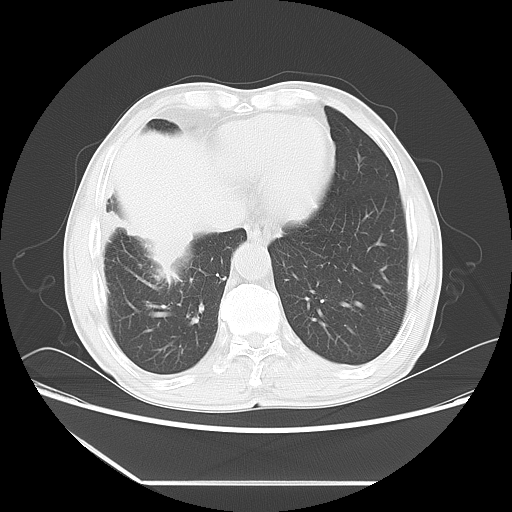
Chest CT, one axial slice; position 18 of 60 along the scan axis; reconstruction kernel LUNG; lung window (W 1500 / L -600 HU); 512 × 512 image matrix, field of view 386 × 386 mm. Patient: male, 72 years. From the clinical record (not read from this slice): clinical TNM (as recorded): T1c N0 M0.
Structures marked on this image (rectangle marked by the reading radiologist):
- lung tumour (recorded histology: squamous cell carcinoma): bounding box (x1, y1, x2, y2) in pixels: (142, 228, 199, 267)